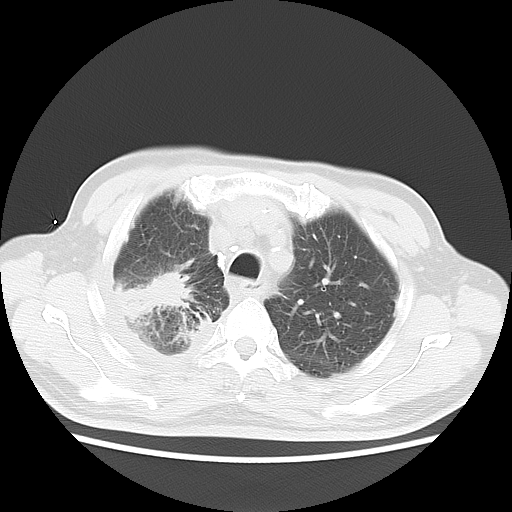
Chest CT, one axial slice; slice 13 of 20 in the series (ordered by position); lung window (W 1500 / L -600 HU); 5 mm slice thickness; 512 × 512 image matrix. Patient: male, 75 years. From the clinical record (not read from this slice): clinical TNM (as recorded): T1c N1 M1.
Outlined on this slice (bounding box drawn by a radiologist):
- lung tumour (recorded histology: adenocarcinoma): bounding box <115,264,203,327> (left, top, right, bottom; pixels)